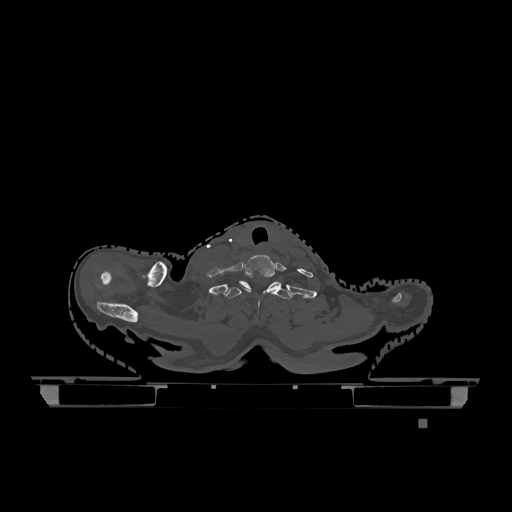
CT including the spine, one axial slice; slice 1013 of 1317 in the series (ordered by position); bone window (W 1800 / L 400 HU); 0.5 mm slice thickness; 512 × 512 image matrix, field of view 500 × 500 mm. Female patient, age 74 years. Case-level facts recorded for this patient, not image findings: primary cancer: lung; vertebrae with lytic lesions (as recorded): T1, T4, T5, T6, L4, L5.
Outlined on this slice (semi-automatically segmented with operator editing):
- T1 vertebra: bounding box (x1, y1, x2, y2) in pixels: (223, 281, 292, 308)